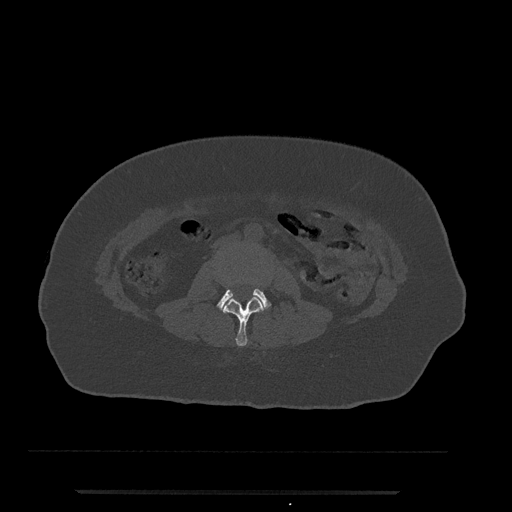
CT including the spine, one axial slice. Position 3 of 797 along the scan axis. Bone window (W 1800 / L 400 HU). 0.5 mm slice thickness. 512 × 512 image matrix, field of view 440 × 440 mm. Female patient, age 51 years. Case-level facts recorded for this patient, not image findings: primary cancer: neuro; vertebrae with lytic lesions (as recorded): T8.
Annotated regions visible in this slice (semi-automatic segmentation, software-assisted and operator-edited):
- L2 vertebra: box from (x=222, y=294) to (x=265, y=346) px